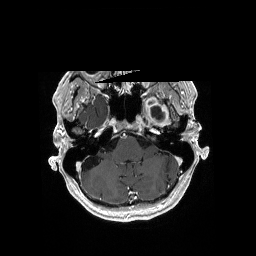
Brain MRI from a brain-tumour surgery series, one axial slice; position 137 of 176 along the scan axis; T1-weighted post-contrast; 1 mm slice thickness; 256 × 256 image matrix. From the clinical record (not read from this slice): histopathology: Glioblastoma; WHO grade: 4; IDH mutation: no.
Annotated regions visible in this slice (outlined manually by an expert reader):
- previous resection cavity: bounding box <150,106,163,118> (left, top, right, bottom; pixels)